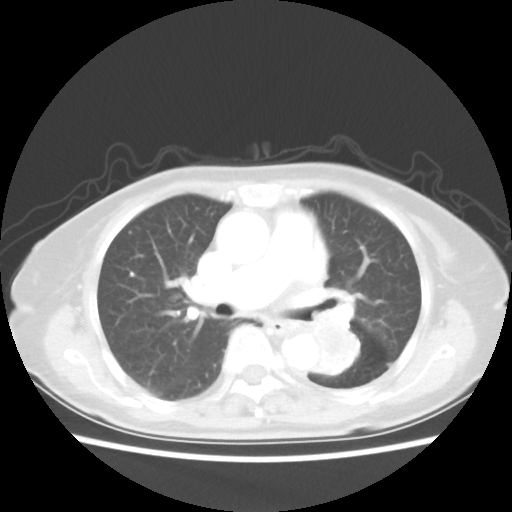
Chest CT, one axial slice; slice 29 of 50 in the series (ordered by position); reconstruction kernel STANDARD; 80 kVp; lung window (W 1500 / L -600 HU); 512 × 512 image matrix, field of view 335 × 335 mm. Female patient, age 81 years. Case-level facts recorded for this patient, not image findings: clinical TNM (as recorded): T2 N0 M1a.
Outlined on this slice (bounding box drawn by a radiologist):
- lung tumour (recorded histology: squamous cell carcinoma): bounding box (x1, y1, x2, y2) in pixels: (304, 315, 363, 380)